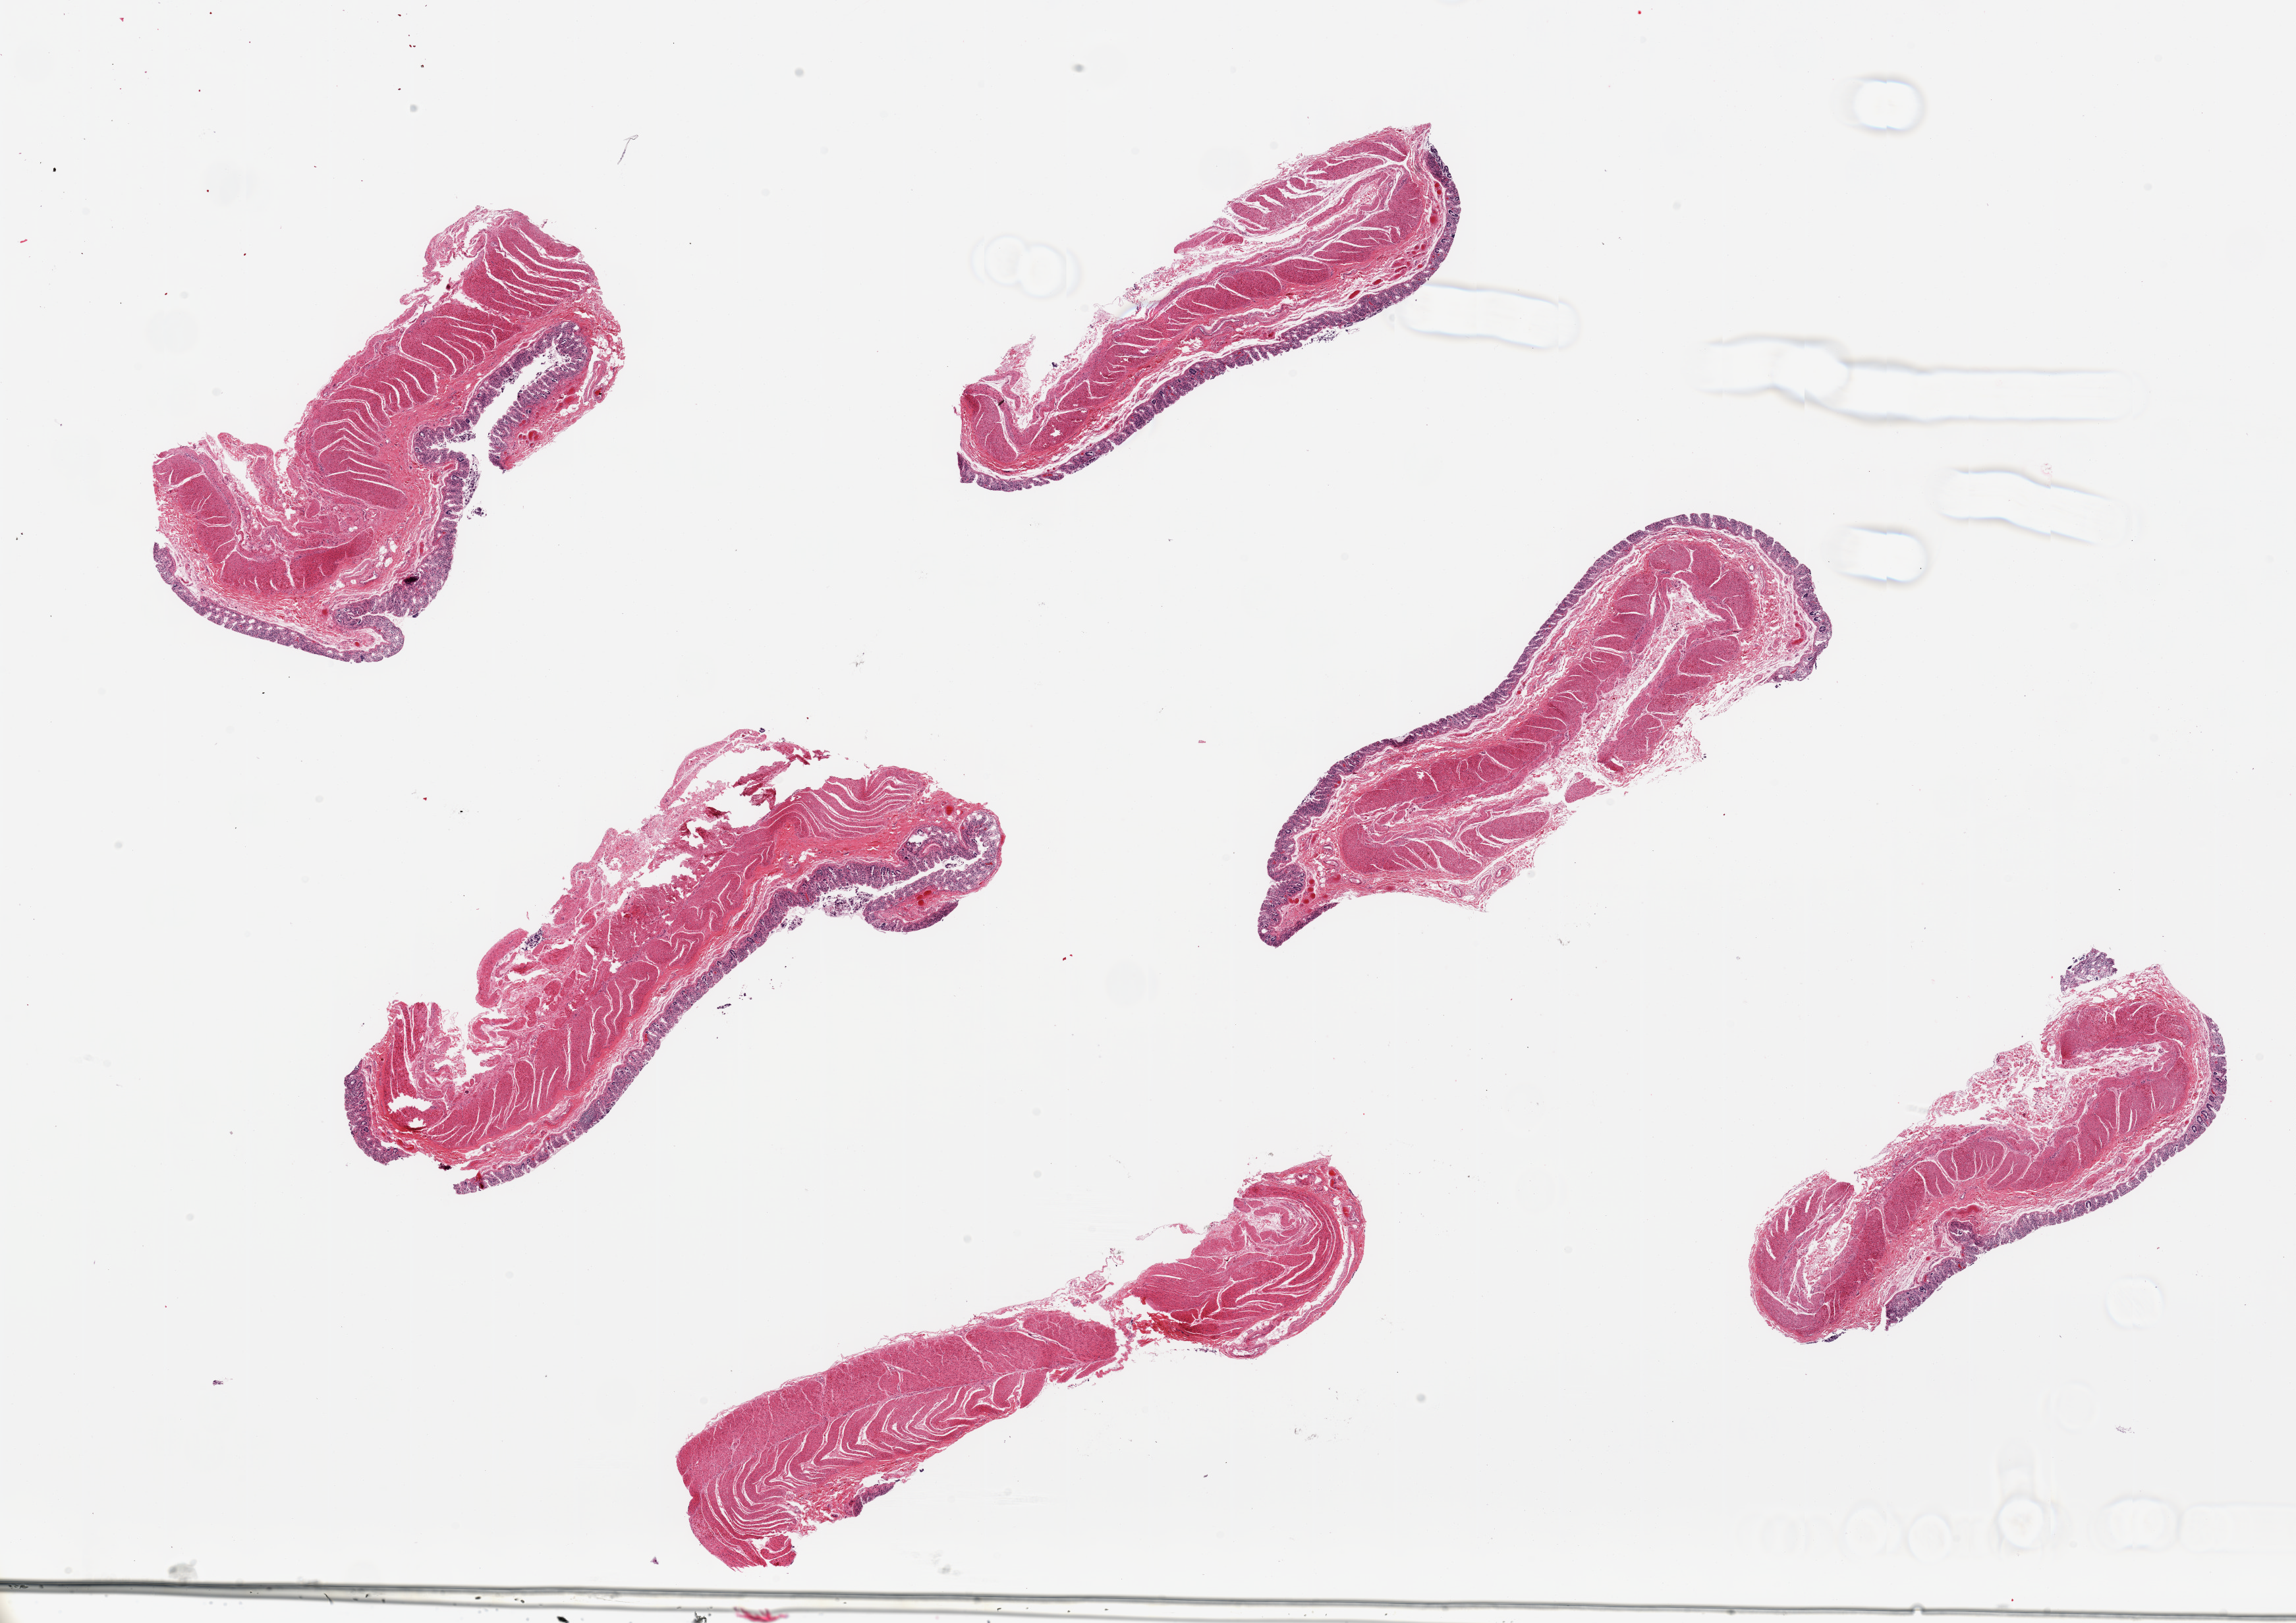
Hematoxylin and eosin (H&E) whole-slide image, low-resolution overview of the scanned area, about 27.6 x 19.5 mm. PAXgene-fixed, paraffin-embedded tissue. Section of transverse colon (target tissue). Donor tissue sample. Male donor.
- pathologist's review note for this sample: 6 ~7x2.5mm pieces. Epithelium totally autolyzed, stroma partially sloughed